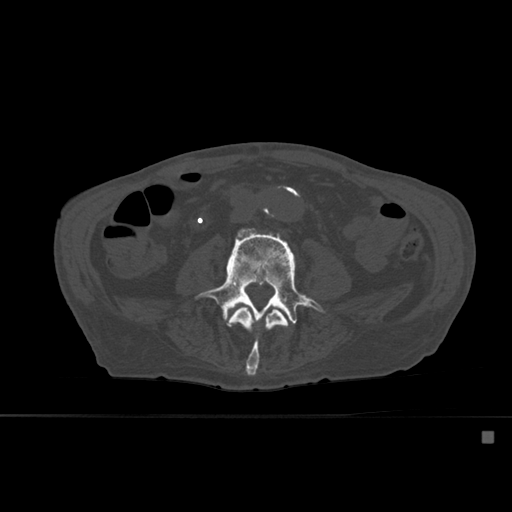
CT including the spine, one axial slice; position 199 of 527 along the scan axis; bone window (W 1800 / L 400 HU); 1.5 mm slice thickness; 512 × 512 image matrix, field of view 373 × 373 mm. Patient: male, 78 years. From the clinical record (not read from this slice): primary cancer: prostate.
Outlined on this slice (semi-automatically segmented with operator editing):
- L3 vertebra: bounding box [x1, y1, x2, y2] px = [227, 306, 288, 376]
- L4 vertebra: [195, 227, 327, 337]